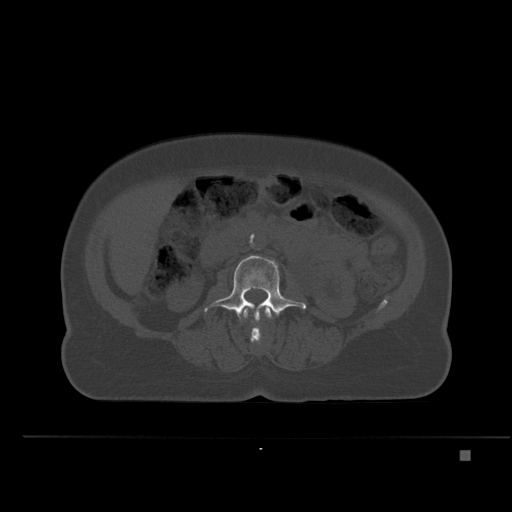
CT including the spine, one axial slice. Position 201 of 477 along the scan axis. Bone window (W 1800 / L 400 HU). 1.5 mm slice thickness. 512 × 512 image matrix, field of view 422 × 422 mm. Female patient, age 74 years. From the clinical record (not read from this slice): primary cancer: colon.
Structures marked on this image (semi-automatic segmentation, software-assisted and operator-edited):
- L2 vertebra: bounding box <243,305,272,344> (left, top, right, bottom; pixels)
- L3 vertebra: <204,255,306,321>